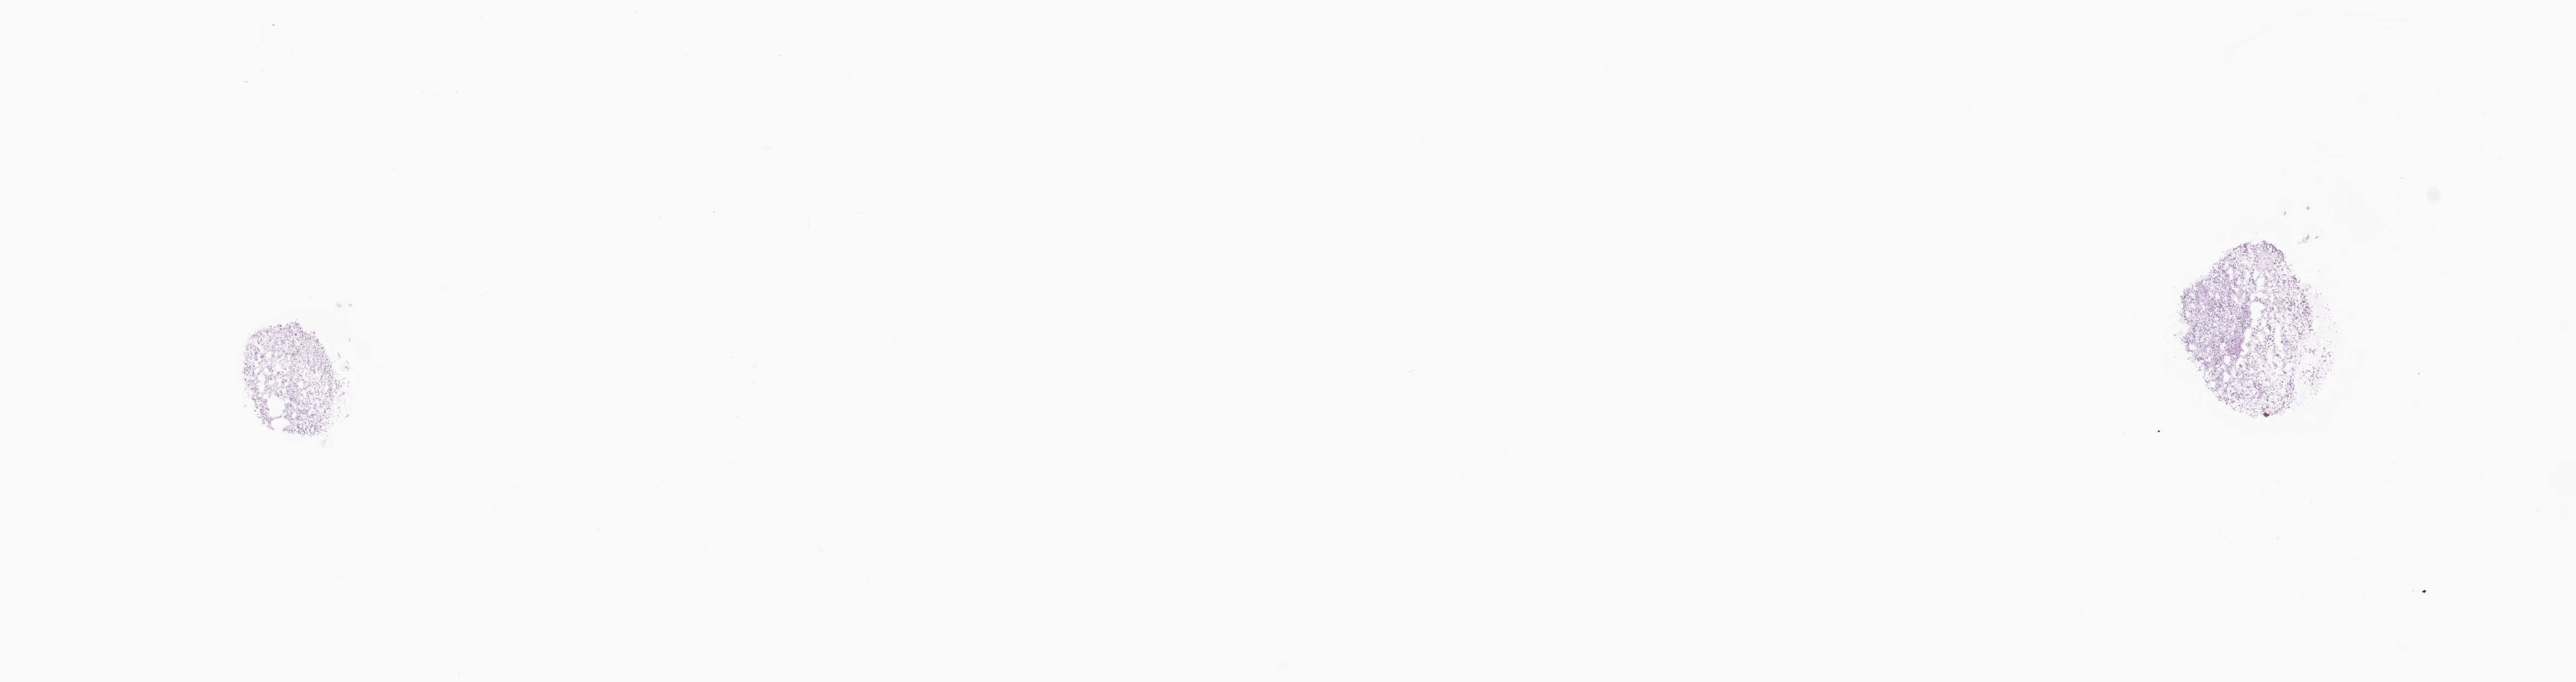
Hematoxylin and eosin (H&E) whole-slide image — low-resolution overview of the scanned area, about 19.8 x 5.2 mm; frozen section; specimen: recurrent tumor; site: brain. Female, age 58 years at initial diagnosis. Composition of this section per pathologist review: tumor cells 96%, tumor nuclei 98%, stromal cells 0%, necrosis 4%, normal cells 0%. Inflammatory infiltration, as recorded: lymphocyte infiltration 0%, monocyte infiltration 0%, neutrophil infiltration 0%.
• patient diagnosis: Glioblastoma, NOS
• section: bottom of the tissue portion